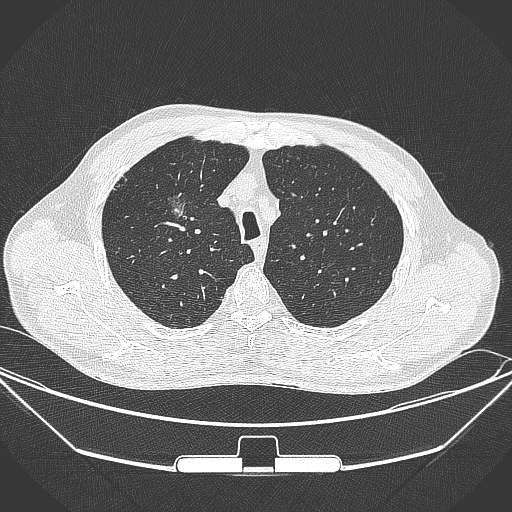
Chest CT, one axial slice; position 270 of 355 along the scan axis; 120 kVp; lung window (W 1500 / L -600 HU); 1 mm slice thickness; 512 × 512 image matrix, field of view 399 × 399 mm. Male patient, age 67 years. Case-level facts recorded for this patient, not image findings: clinical TNM (as recorded): T1c N0 M0; histopathological grade: G2.
Structures marked on this image (bounding box drawn by a radiologist):
- lung tumour (recorded histology: adenocarcinoma): box from (x=163, y=178) to (x=199, y=240) px